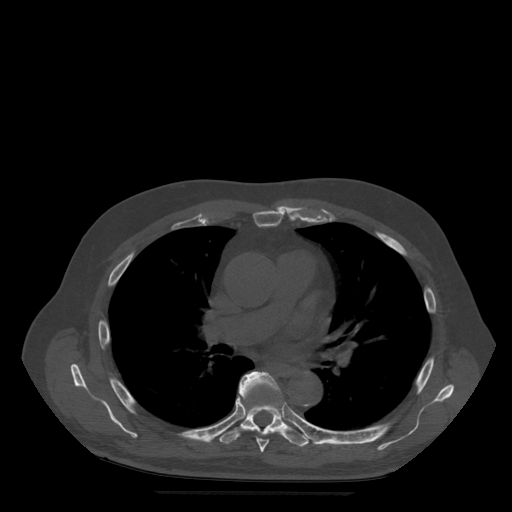
CT including the spine, one axial slice; position 342 of 522 along the scan axis; bone window (W 1800 / L 400 HU); 1.25 mm slice thickness; 512 × 512 image matrix, field of view 420 × 420 mm. Patient age 72 years. From the clinical record (not read from this slice): primary cancer: prostate.
Annotated regions visible in this slice (semi-automatically segmented with operator editing):
- T6 vertebra: bounding box [x1, y1, x2, y2] px = [239, 372, 283, 453]
- T7 vertebra: [218, 390, 310, 447]